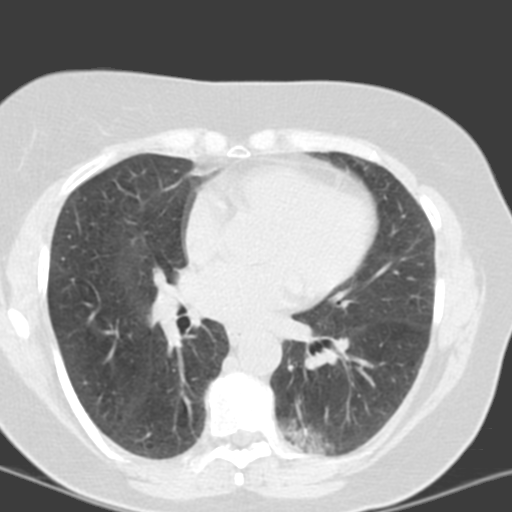
Axial slice from a low-dose chest CT screening exam. Third screening round (two years after baseline). Lung window (W 1500 / L -600 HU). Standard (soft-tissue) reconstruction kernel (B). Slice 71 of 150 in the series. Female, age 55 years at enrolment. Current smoker at enrolment.
Expert reader's lesion annotation, box from (x=278, y=404) to (x=359, y=461) px. The screening reader recorded 6 non-calcified nodules or masses ≥4 mm on this exam (left lower lobe, left lower lobe, left upper lobe, lingula, lingula, right middle lobe); which of them this box marks is not recorded. Official screen result: positive, no significant change: stable abnormalities potentially related to lung cancer, unchanged since the prior screening exam. Later outcome: lung cancer diagnosed 357 days after this screen — adenocarcinoma with mixed subtypes, left lower lobe, poorly differentiated (G3), stage IA (AJCC 6th edition), 21 mm at pathology.